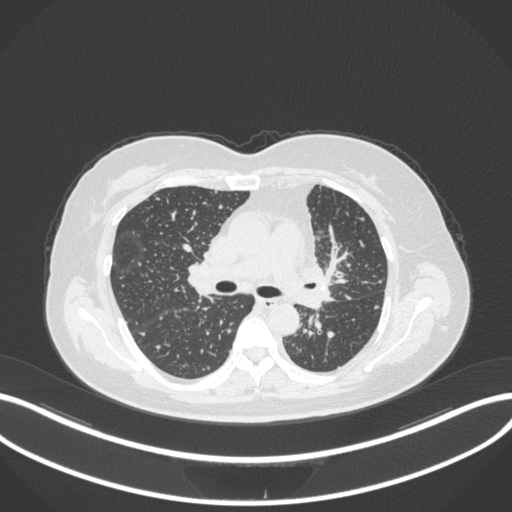
Chest CT, one axial slice; position 204 of 348 along the scan axis; reconstruction kernel B31f; 120 kVp; lung window (W 1500 / L -600 HU); 1 mm slice thickness; 512 × 512 image matrix. Female patient, age 49 years. From the clinical record (not read from this slice): clinical TNM (as recorded): T1c N0 M1.
Outlined on this slice (rectangle marked by the reading radiologist):
- lung tumour (recorded histology: adenocarcinoma): bounding box [x1, y1, x2, y2] px = [288, 252, 340, 314]